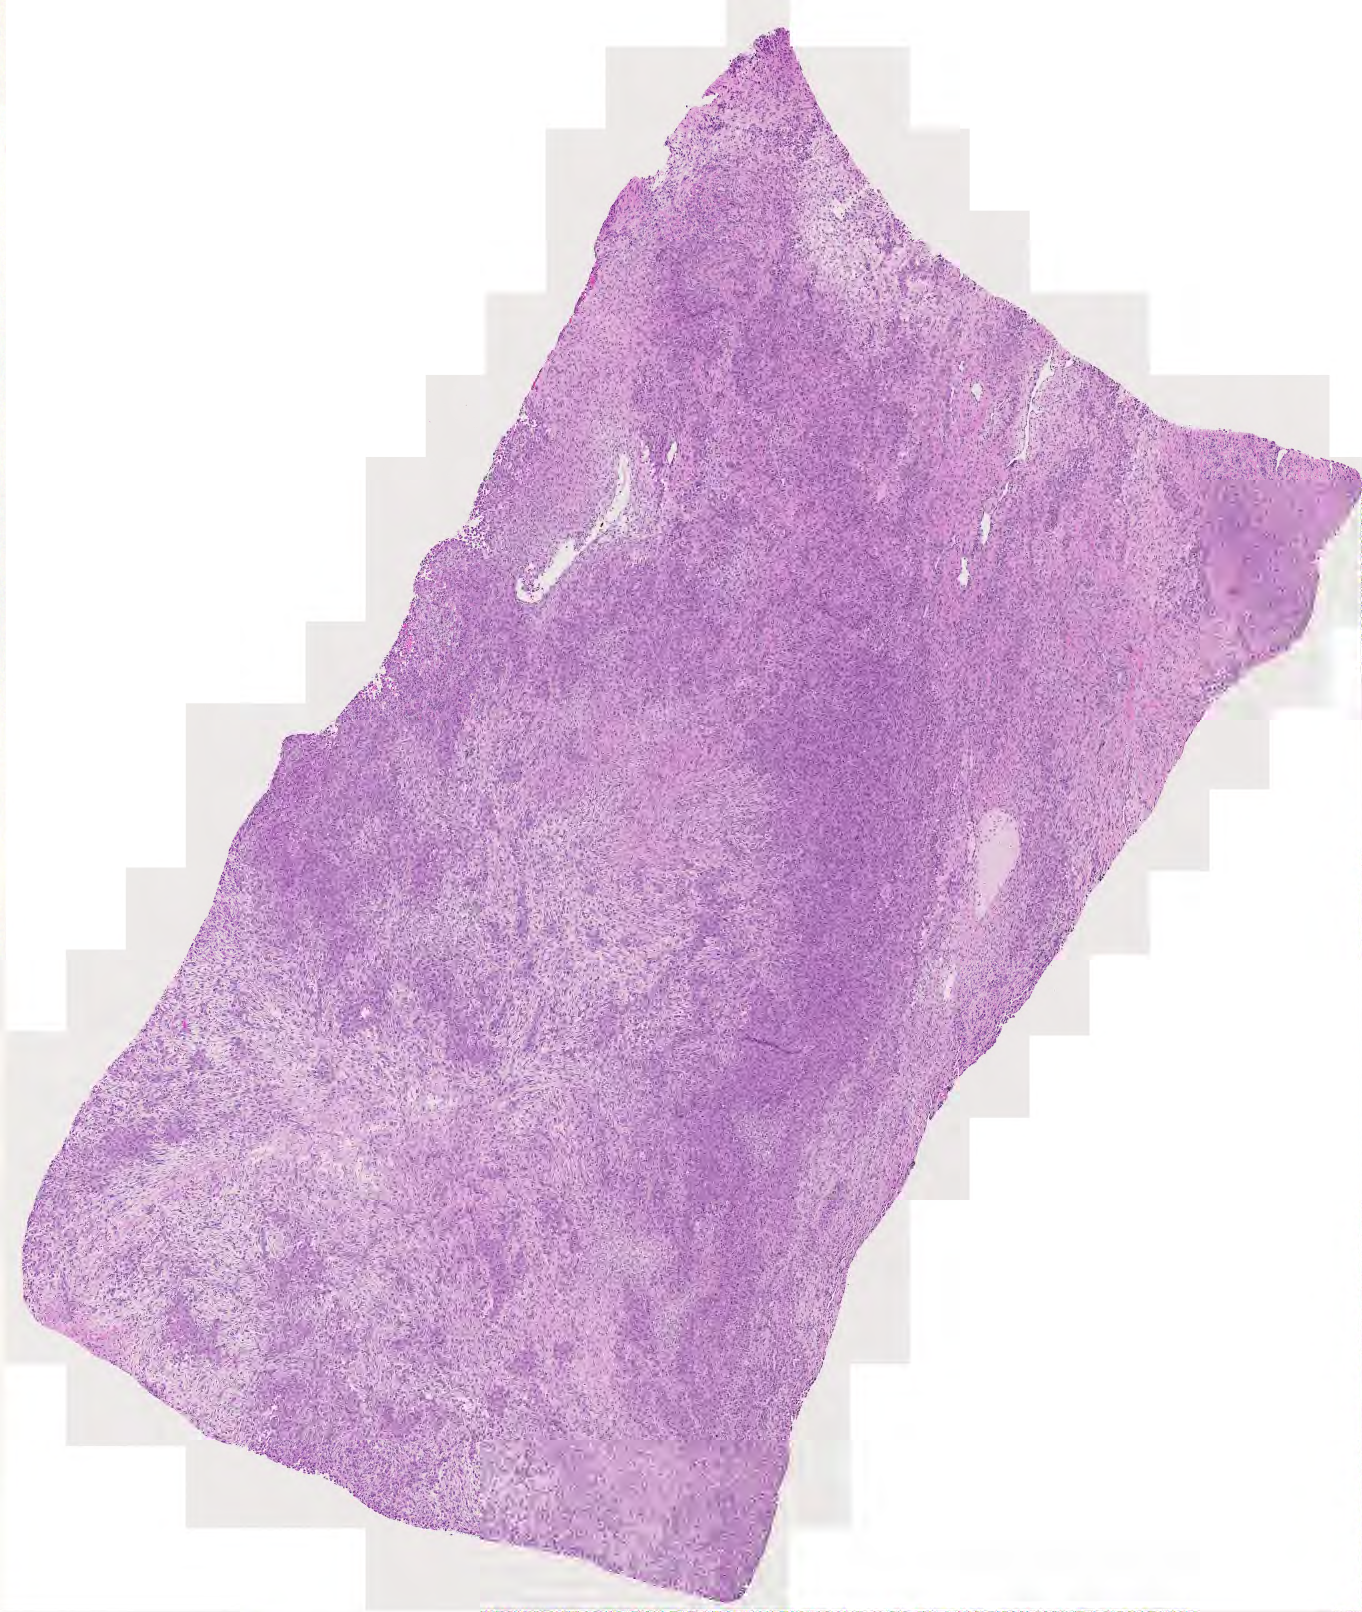
Digitized H&E tissue section (whole slide), whole scanned area (about 7.0 x 8.3 mm, from a 20x scan) shown as a low-resolution overview; tumour tissue sample. Male, 49 y/o.
* primary tumour site (as recorded): upper extremity
* patient diagnosis (cohort enrolment): sarcoma (site not recorded at cohort level)